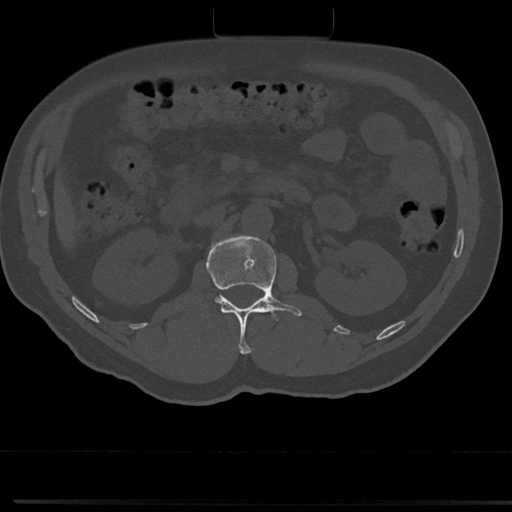
CT including the spine, one axial slice; reconstruction kernel Br40s/3; bone window (W 1800 / L 400 HU); 512 × 512 image matrix. Male patient, age 61 years. From the clinical record (not read from this slice): primary cancer: prostate.
Annotated regions visible in this slice (semi-automatic segmentation, software-assisted and operator-edited):
- L1 vertebra: bounding box [x1, y1, x2, y2] px = [208, 235, 302, 354]